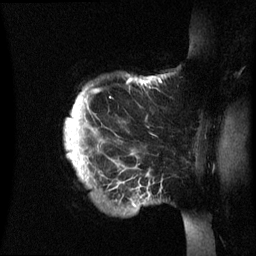
Breast MRI (dynamic contrast-enhanced), one sagittal slice; dynamic contrast-enhanced series, image 2 of 3 at this slice position (ordered by acquisition); 1.5 T; TE 4.2 ms, TR 8.4 ms; 256 × 256 image matrix. Patient: female, 48 years.
Structures marked on this image (semi-automatic segmentation, software-assisted and operator-edited):
- analysis volume of interest (the breast-tissue region the enhancement analysis was run in; not a lesion): bounding box (x1, y1, x2, y2) in pixels: (65, 75, 195, 236)
- tumour enhancement mask (voxels above the 70 % enhancement threshold inside the analysis volume of interest): (73, 81, 148, 170)